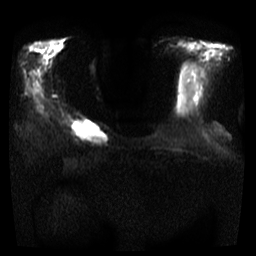
Breast MRI, one axial slice; slice 9 of 35 in the series (ordered by position); diffusion-weighted series; image 2 of 4 stored at this slice position (different b-values; order by instance number); 3 T; 5 mm slice thickness; 256 × 256 image matrix, field of view 300 × 300 mm. Female patient.
Outlined on this slice (outlined manually by an expert reader):
- tumour on diffusion-weighted imaging: bounding box [x1, y1, x2, y2] px = [69, 118, 109, 143]